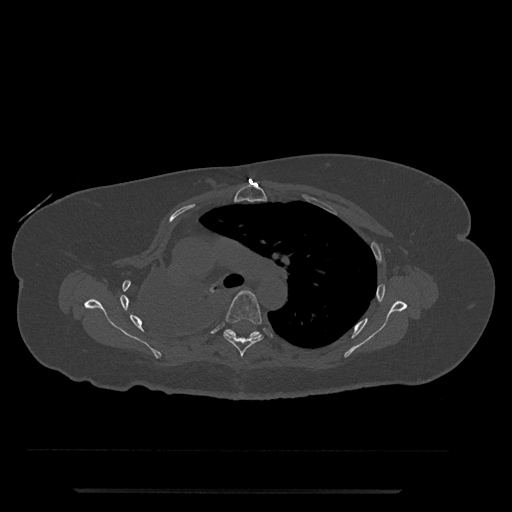
CT including the spine, one axial slice. Position 533 of 797 along the scan axis. Reconstruction kernel Br40s/3. Bone window (W 1800 / L 400 HU). 0.5 mm slice thickness. 512 × 512 image matrix, field of view 440 × 440 mm. Female patient, age 51 years. From the clinical record (not read from this slice): primary cancer: neuro; vertebrae with lytic lesions (as recorded): T8.
Annotated regions visible in this slice (semi-automatic segmentation, software-assisted and operator-edited):
- T5 vertebra: bounding box (x1, y1, x2, y2) in pixels: (223, 290, 263, 357)
- T6 vertebra: (224, 329, 261, 338)